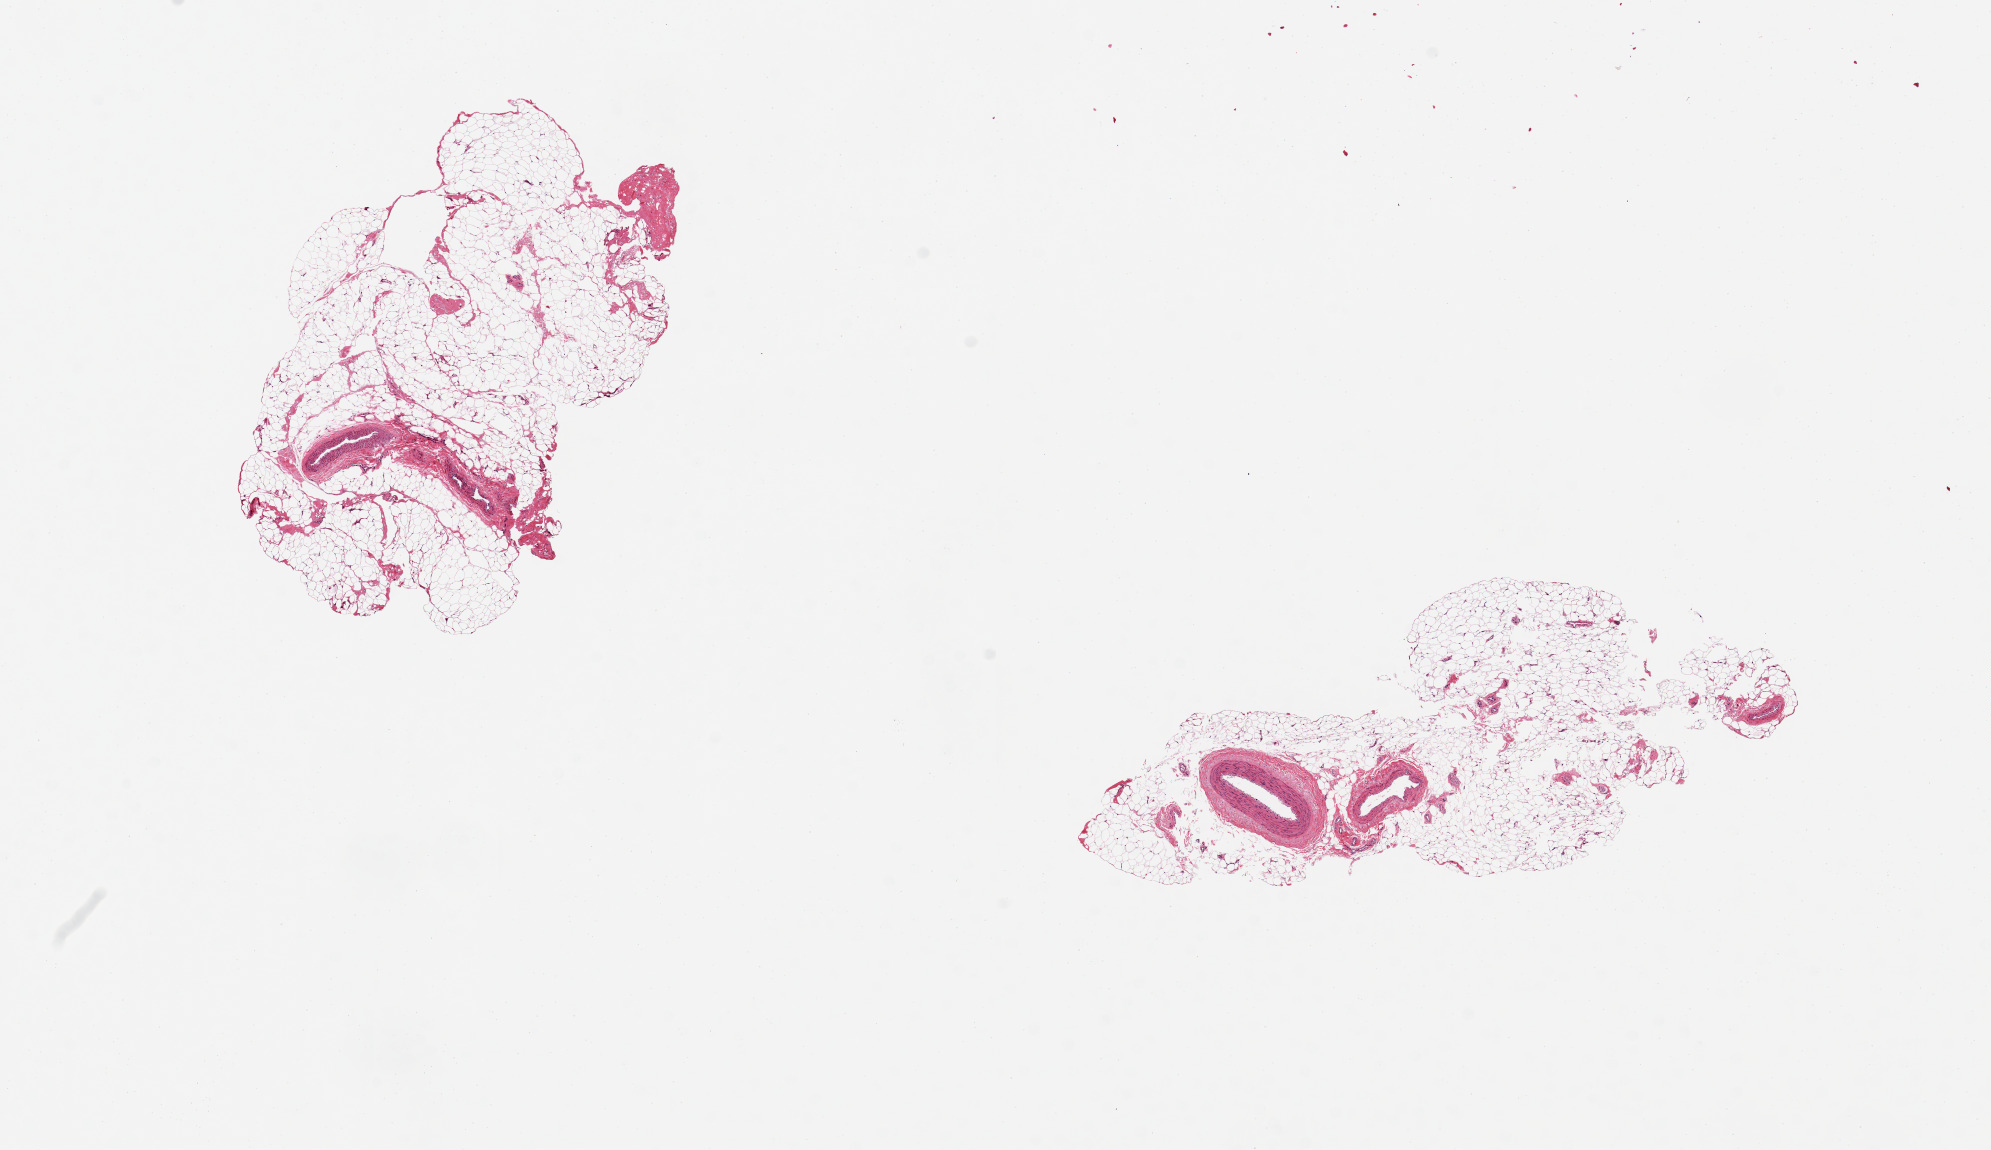
Digitized haematoxylin and eosin-stained section, whole scanned area (about 15.8 x 9.1 mm, from a 20x scan) shown as a low-resolution overview, PAXgene-fixed, paraffin-embedded tissue, sampled site (target tissue): tibial artery, donor tissue sample. Female donor.
• pathologist's review note for this sample: 2 pieces 5x2 & 4x2 mm; small vessels, arteries and veins, (1x0.6 mm & 0.8 mm) embedded in ~60 & ~90% adipose